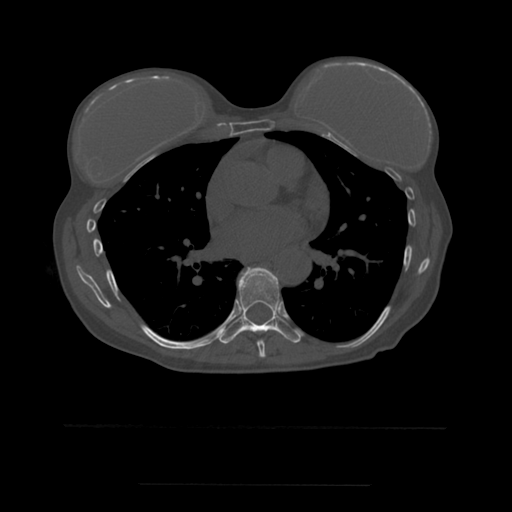
CT including the spine, one axial slice. Slice 345 of 544 in the series (ordered by position). Bone window (W 1800 / L 400 HU). 512 × 512 image matrix, field of view 350 × 350 mm. Patient age 58 years. Case-level facts recorded for this patient, not image findings: primary cancer: lung.
Outlined on this slice (semi-automatically segmented with operator editing):
- T7 vertebra: bounding box [x1, y1, x2, y2] px = [257, 272, 279, 358]
- T8 vertebra: [220, 267, 302, 344]